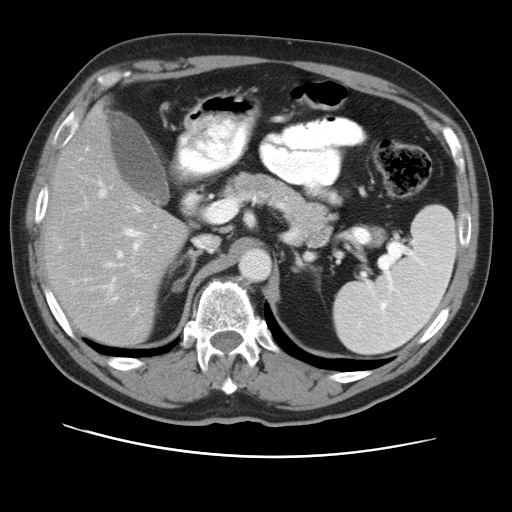
Contrast-enhanced abdominal CT, one axial slice. Position 28 of 49 along the scan axis. Reconstruction kernel STANDARD. Intravenous contrast given. Soft-tissue window (W 400 / L 40 HU). 512 × 512 image matrix, field of view 374 × 374 mm. Male patient, age 59 years. Case-level facts recorded for this patient, not image findings: diagnosis: colorectal cancer liver metastases, imaged before liver resection; multiple liver metastases: yes; largest metastasis: 6.3 cm.
Annotated regions visible in this slice (expert manual segmentation):
- hepatic veins: box from (x=100, y=182) to (x=212, y=249) px
- liver: (x=46, y=110)–(x=186, y=345)
- planned liver remnant (the part of the liver to remain after resection): (x=47, y=110)–(x=186, y=345)
- portal vein (with intrahepatic branches): (x=105, y=228)–(x=140, y=300)